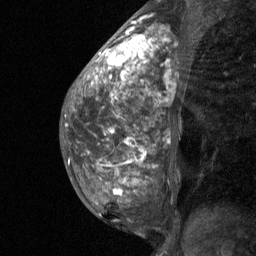
Breast MRI (dynamic contrast-enhanced), one sagittal slice; position 27 of 64 along the scan axis; dynamic contrast-enhanced study with each time point stored as its own series, time point 2 of 3 at this slice position (early post-contrast, ordered by acquisition time); 1.5 T; TE 4.8 ms, TR 27 ms; 2 mm slice thickness; 256 × 256 image matrix, field of view 180 × 180 mm. Female patient, age 36 years. Case-level facts recorded for this patient, not image findings: setting: breast cancer imaged before/during neoadjuvant chemotherapy; receptor status: HR-positive, HER2-negative.
Annotated regions visible in this slice (semi-automatic segmentation, software-assisted and operator-edited):
- analysis volume of interest (the breast-tissue region the enhancement analysis was run in; not a lesion): box from (x=67, y=12) to (x=189, y=238) px
- tumour enhancement mask (voxels above the 90 % enhancement threshold inside the analysis volume of interest): (x=92, y=22)–(x=158, y=194)